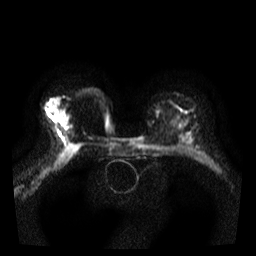
Breast MRI, one axial slice; slice 23 of 35 in the series (ordered by position); diffusion-weighted series; image 2 of 4 stored at this slice position (different b-values; order by instance number); 3 T; 5 mm slice thickness; 256 × 256 image matrix, field of view 300 × 300 mm. Female patient.
Structures marked on this image (manually delineated by an expert):
- tumour on diffusion-weighted imaging: box from (x=54, y=118) to (x=56, y=120) px